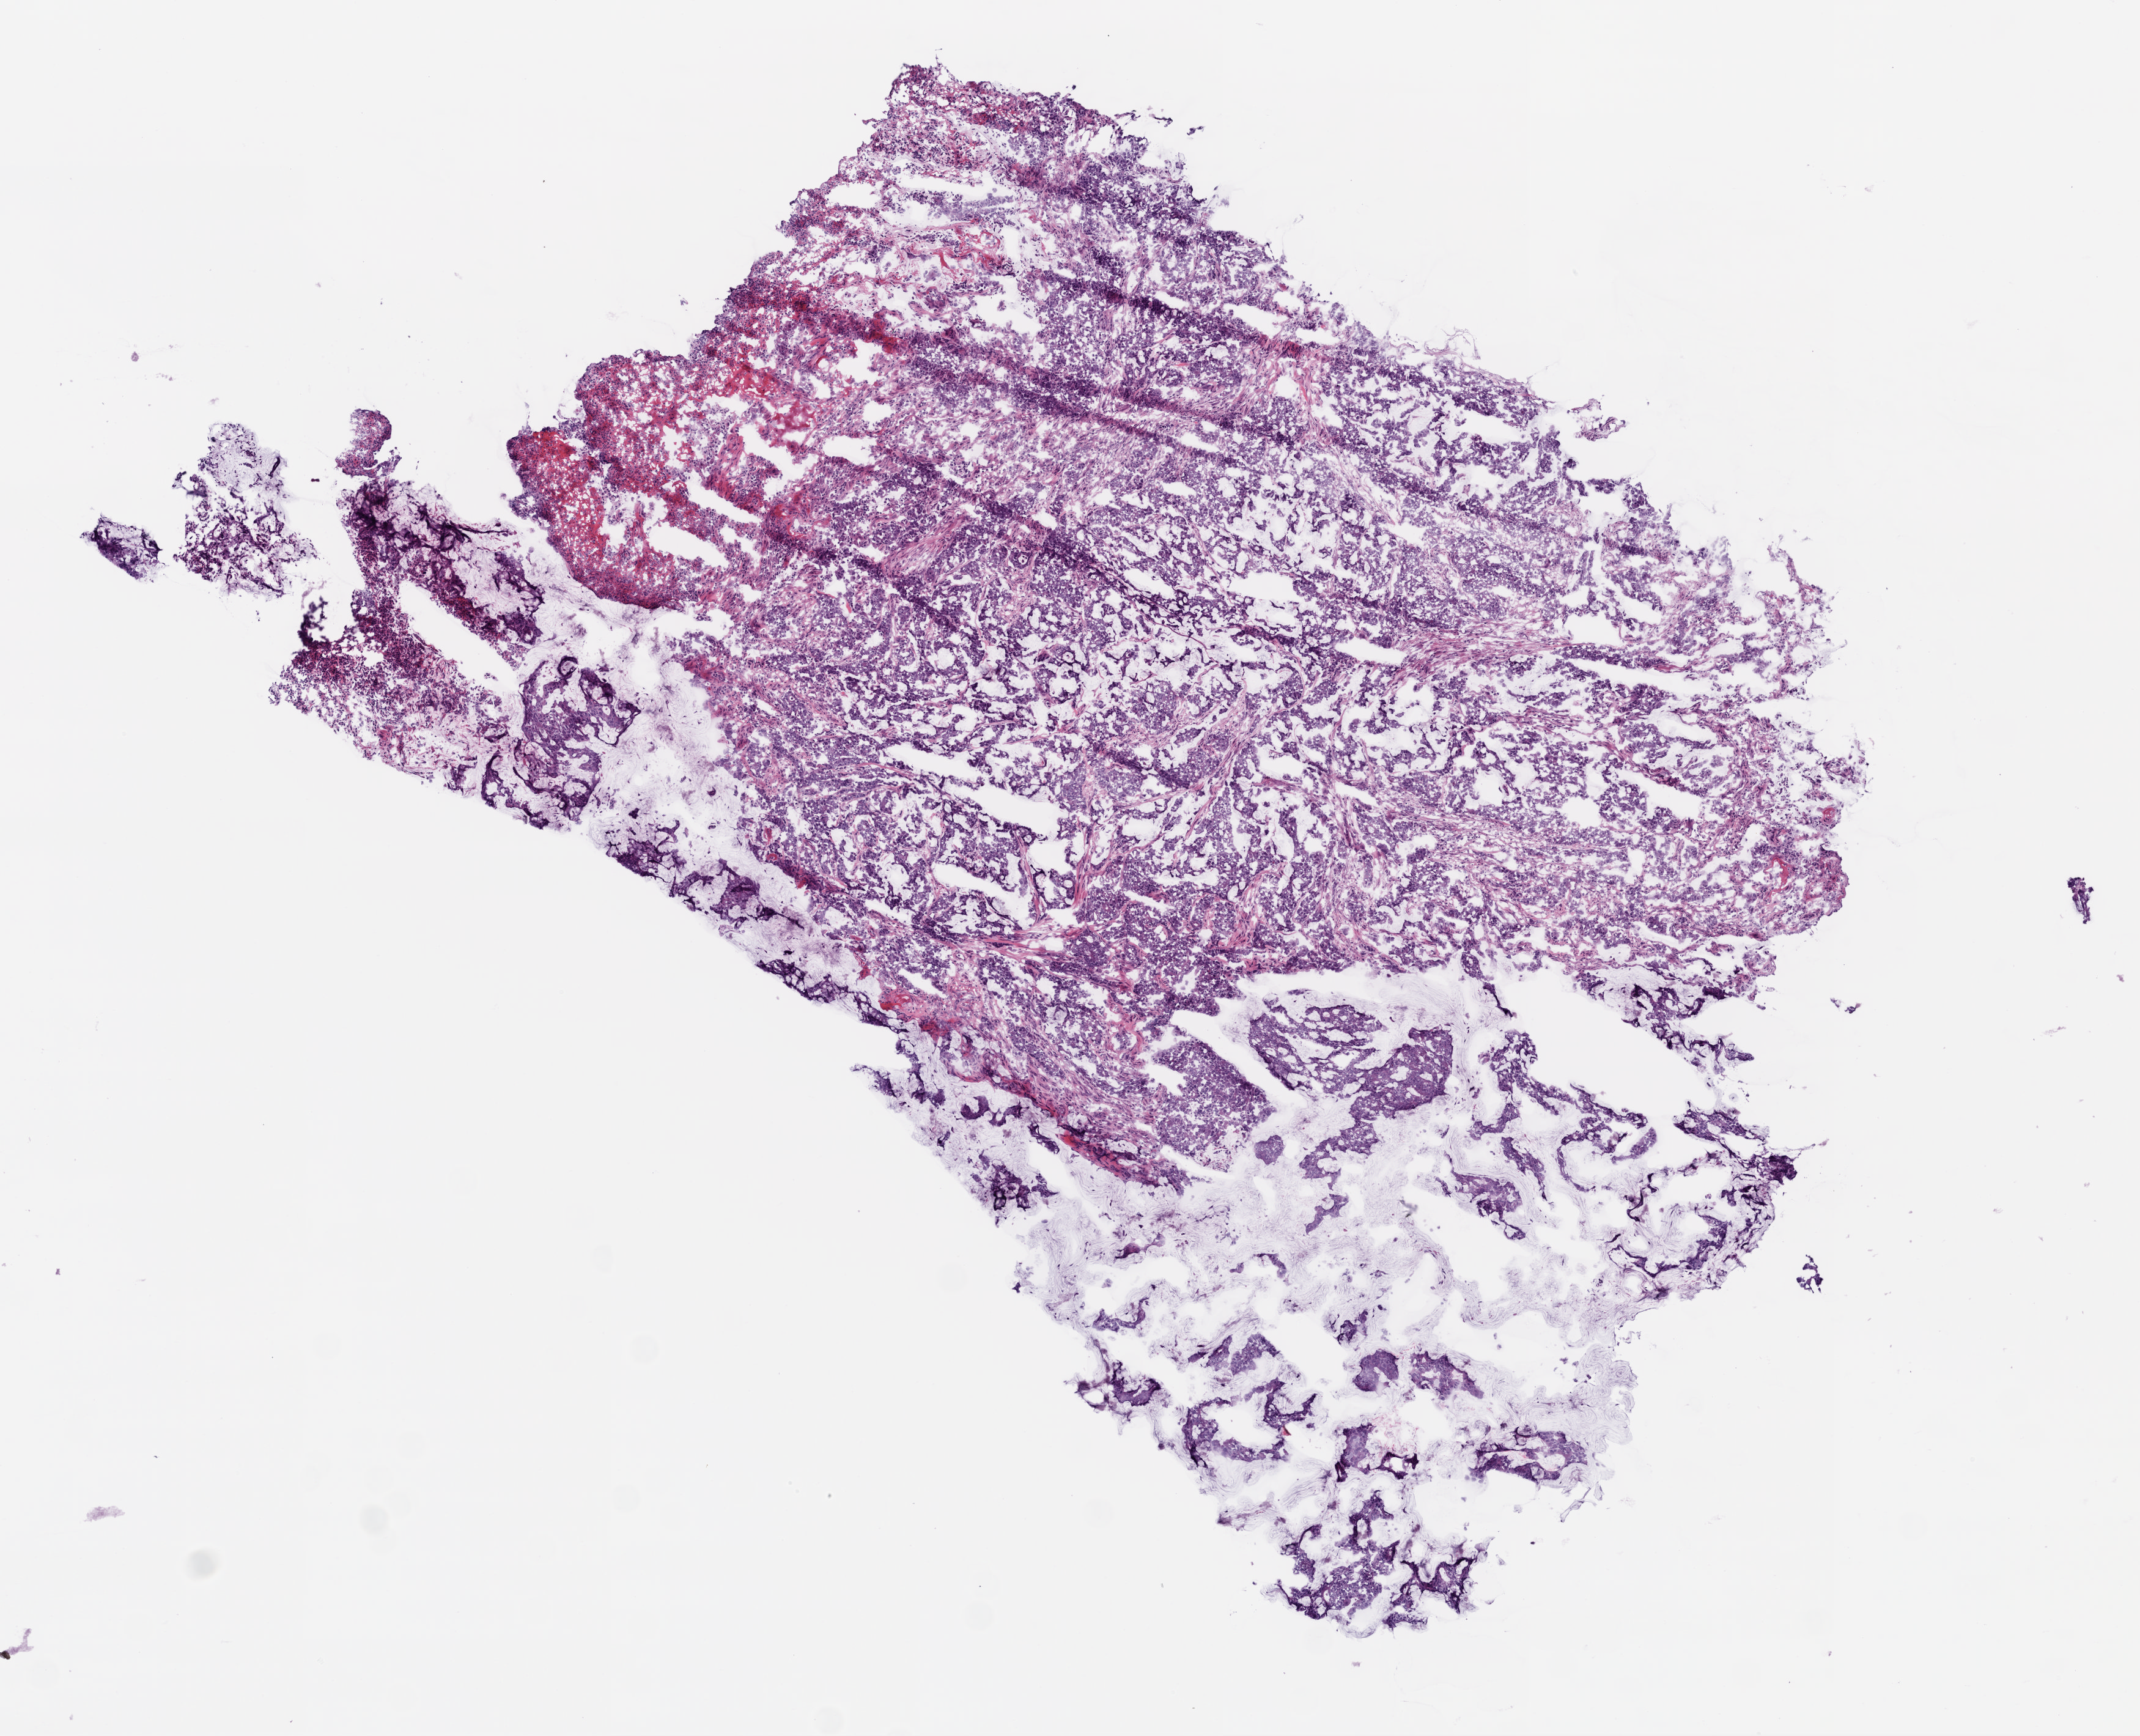
Digitized H&E tissue section (whole slide) — low-resolution overview of the scanned area, about 7.0 x 5.7 mm (acquisition: 20x scan). Frozen section from the bottom of the tissue portion. Colon, primary tumour sample. Female patient; age at initial diagnosis 79 years. Composition of this section per pathologist review: tumour cells 80%, tumour nuclei 85%, normal cells 0%, stromal cells 10%, necrosis 10%.
• histologic diagnosis: Mucinous adenocarcinoma (ascending colon)
• AJCC pathologic stage: IIA (6th edition)